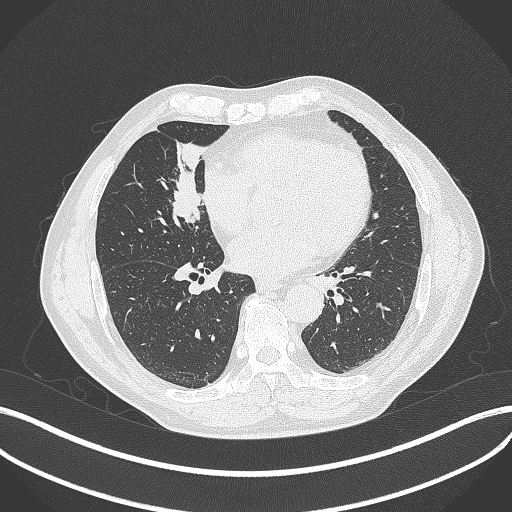
Chest CT, one axial slice; slice 167 of 429 in the series (ordered by position); reconstruction kernel B70f; 120 kVp; lung window (W 1500 / L -600 HU); 1 mm slice thickness; 512 × 512 image matrix, field of view 400 × 400 mm. Male patient, age 61 years. Case-level facts recorded for this patient, not image findings: clinical TNM (as recorded): T2b N1 M0.
Outlined on this slice (rectangle marked by the reading radiologist):
- lung tumour (recorded histology: squamous cell carcinoma): bounding box <169,164,213,236> (left, top, right, bottom; pixels)